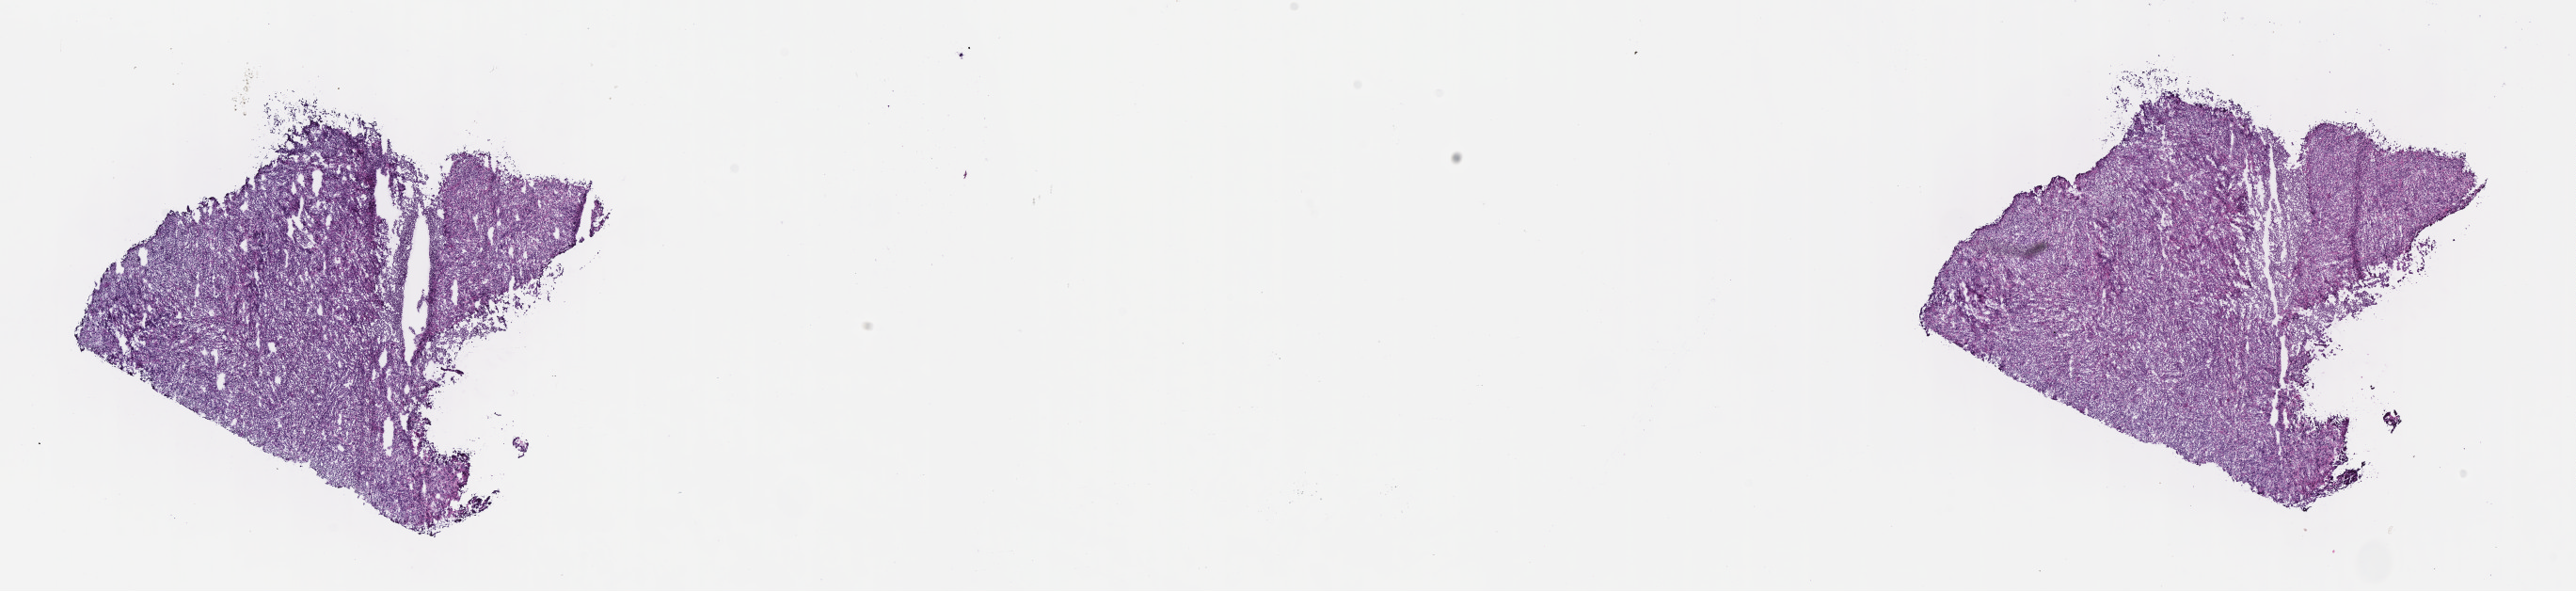
Whole-slide image, haematoxylin and eosin stain — low-resolution overview of the scanned area, about 22.1 x 5.1 mm, cryosection, primary tumor, site: soft tissue. Patient: female, age at initial diagnosis 9 years. Slide review estimates, as recorded: tumor cells 90%, tumor nuclei 95%, stromal cells 5%, necrosis 5%, normal cells 0%. Inflammatory infiltration, as recorded: lymphocyte infiltration 3%, monocyte infiltration 3%, neutrophil infiltration 0%.
Histologic diagnosis: Burkitt lymphoma, NOS. Ann Arbor stage (patient): Stage III.